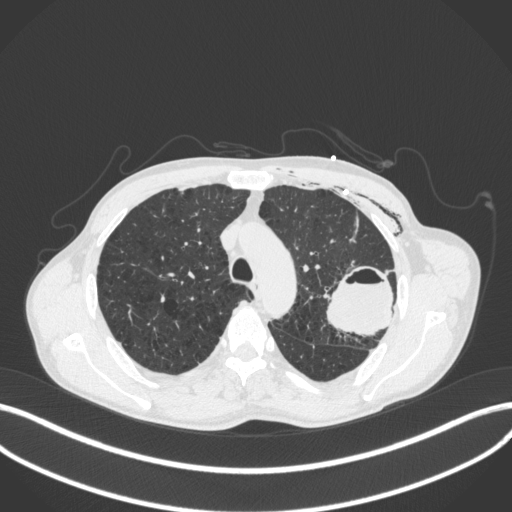
Chest CT, one axial slice; reconstruction kernel B31f; 120 kVp; lung window (W 1500 / L -600 HU); 1 mm slice thickness; 512 × 512 image matrix, field of view 400 × 400 mm. Patient: male, 58 years. From the clinical record (not read from this slice): clinical TNM (as recorded): T3 N0 M0.
Outlined on this slice (bounding box drawn by a radiologist):
- lung tumour (recorded histology: adenocarcinoma): bounding box (x1, y1, x2, y2) in pixels: (327, 266, 398, 337)